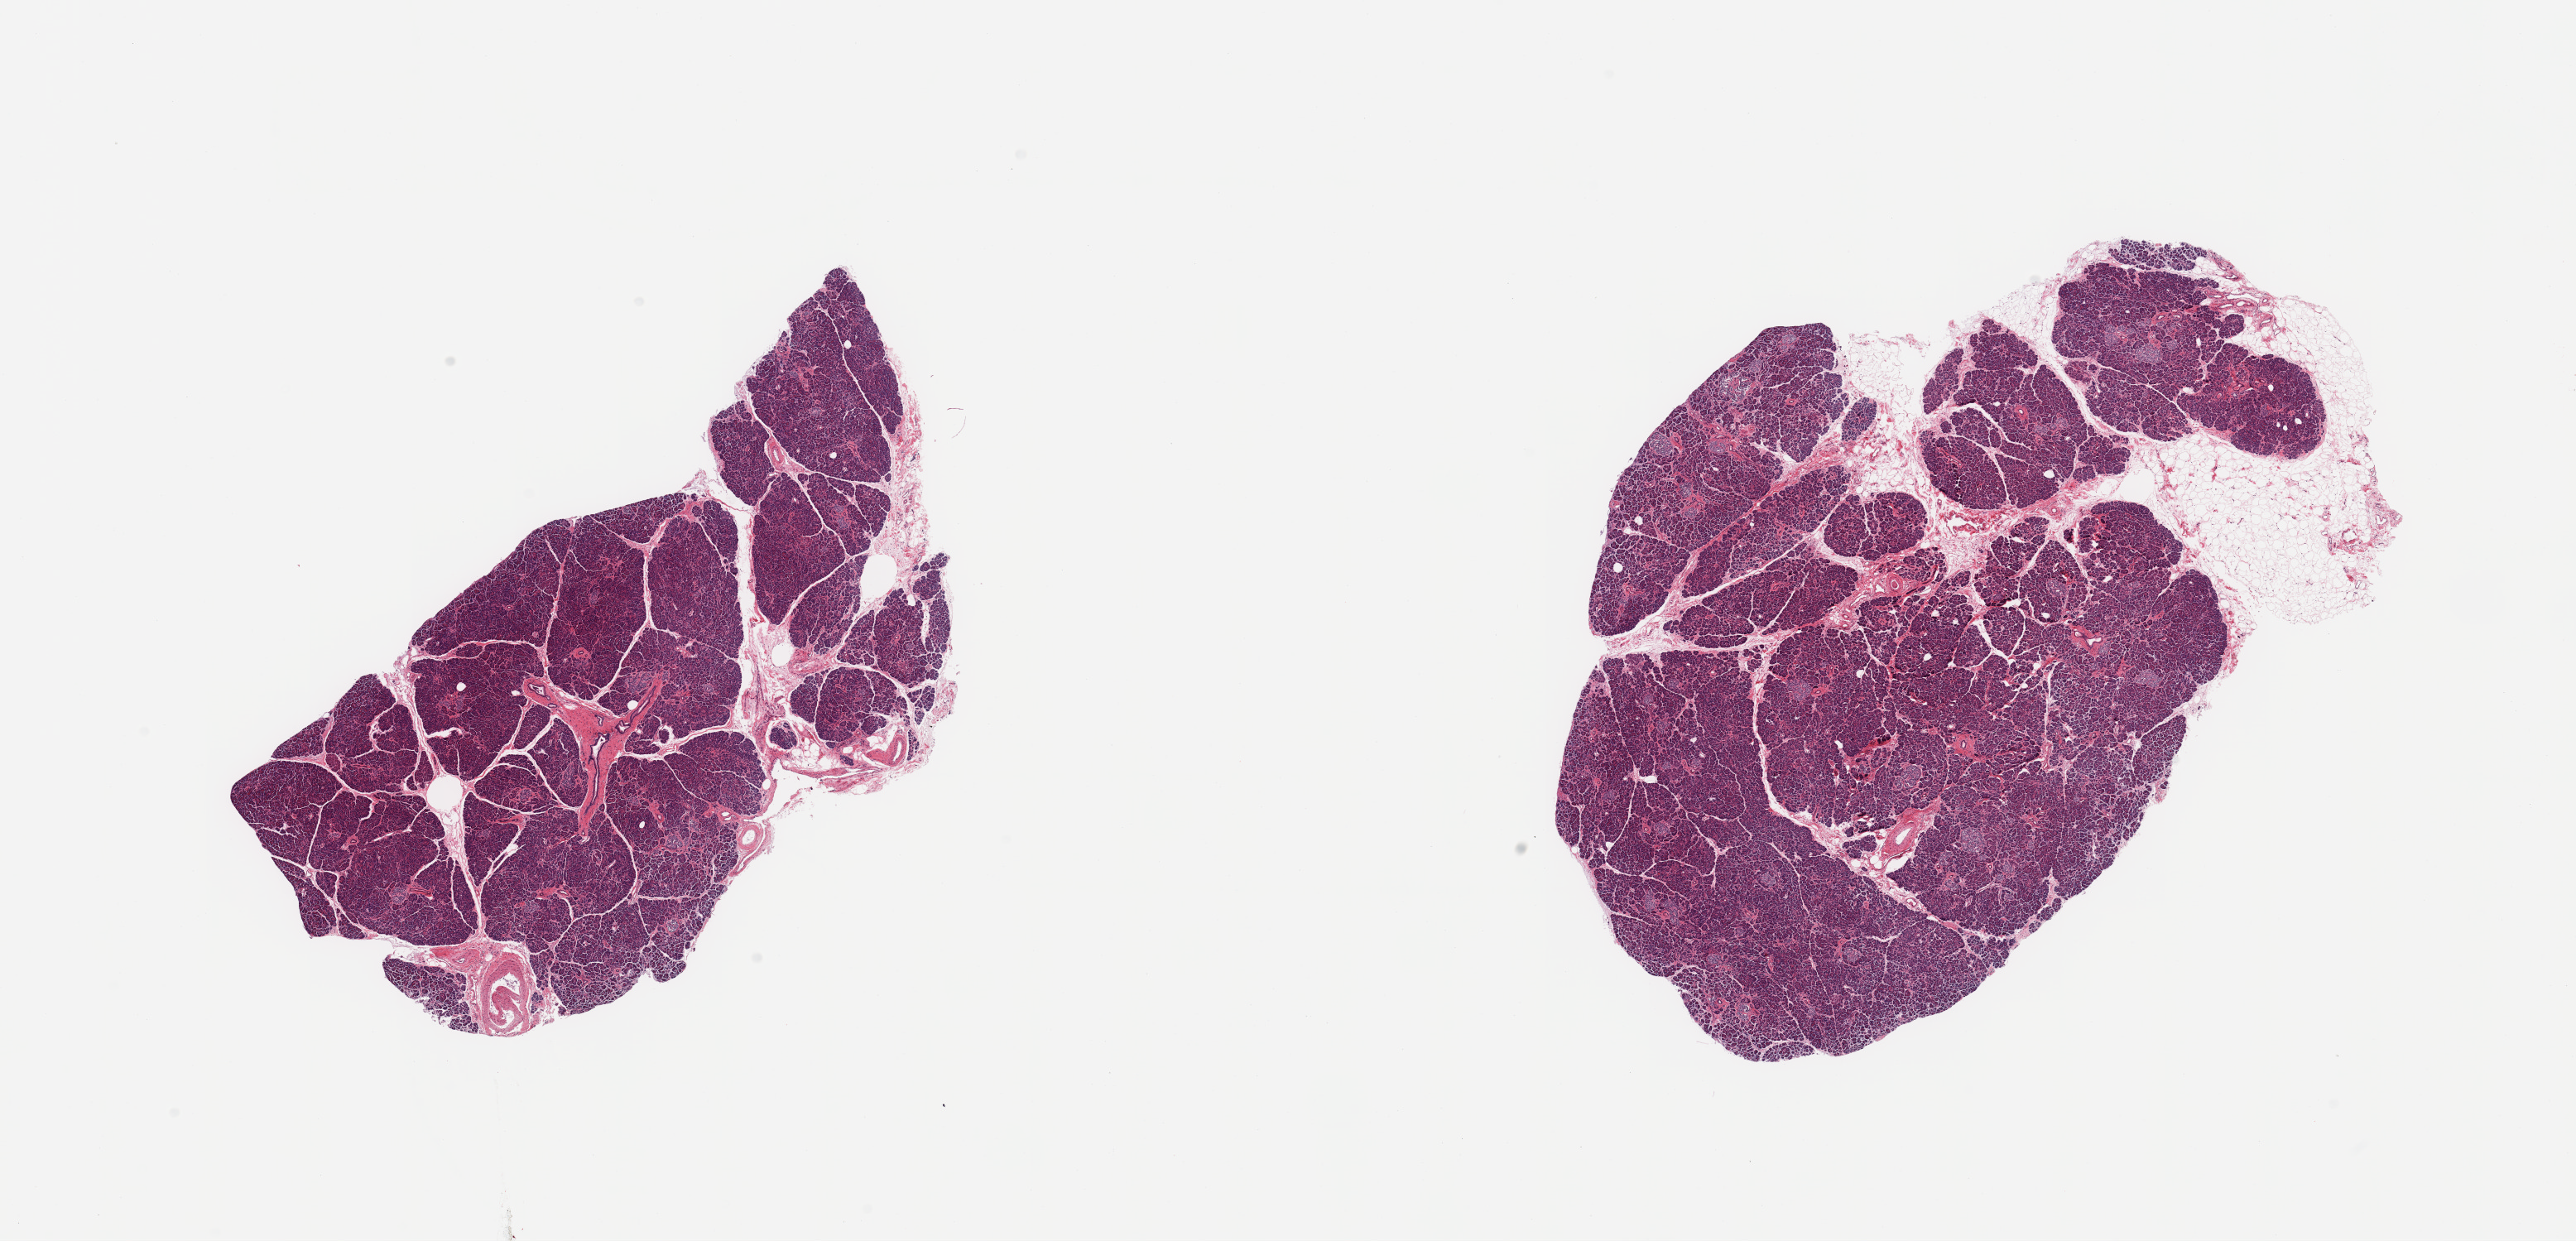
Whole-slide image, haematoxylin and eosin stain, low-resolution overview of the scanned area, about 24.6 x 11.9 mm; PAXgene-fixed paraffin-embedded (PFPE) section; section of pancreas (target tissue); tissue donor sample.
• reviewer comment on this tissue sample: 2 pieces, well fixed Islets